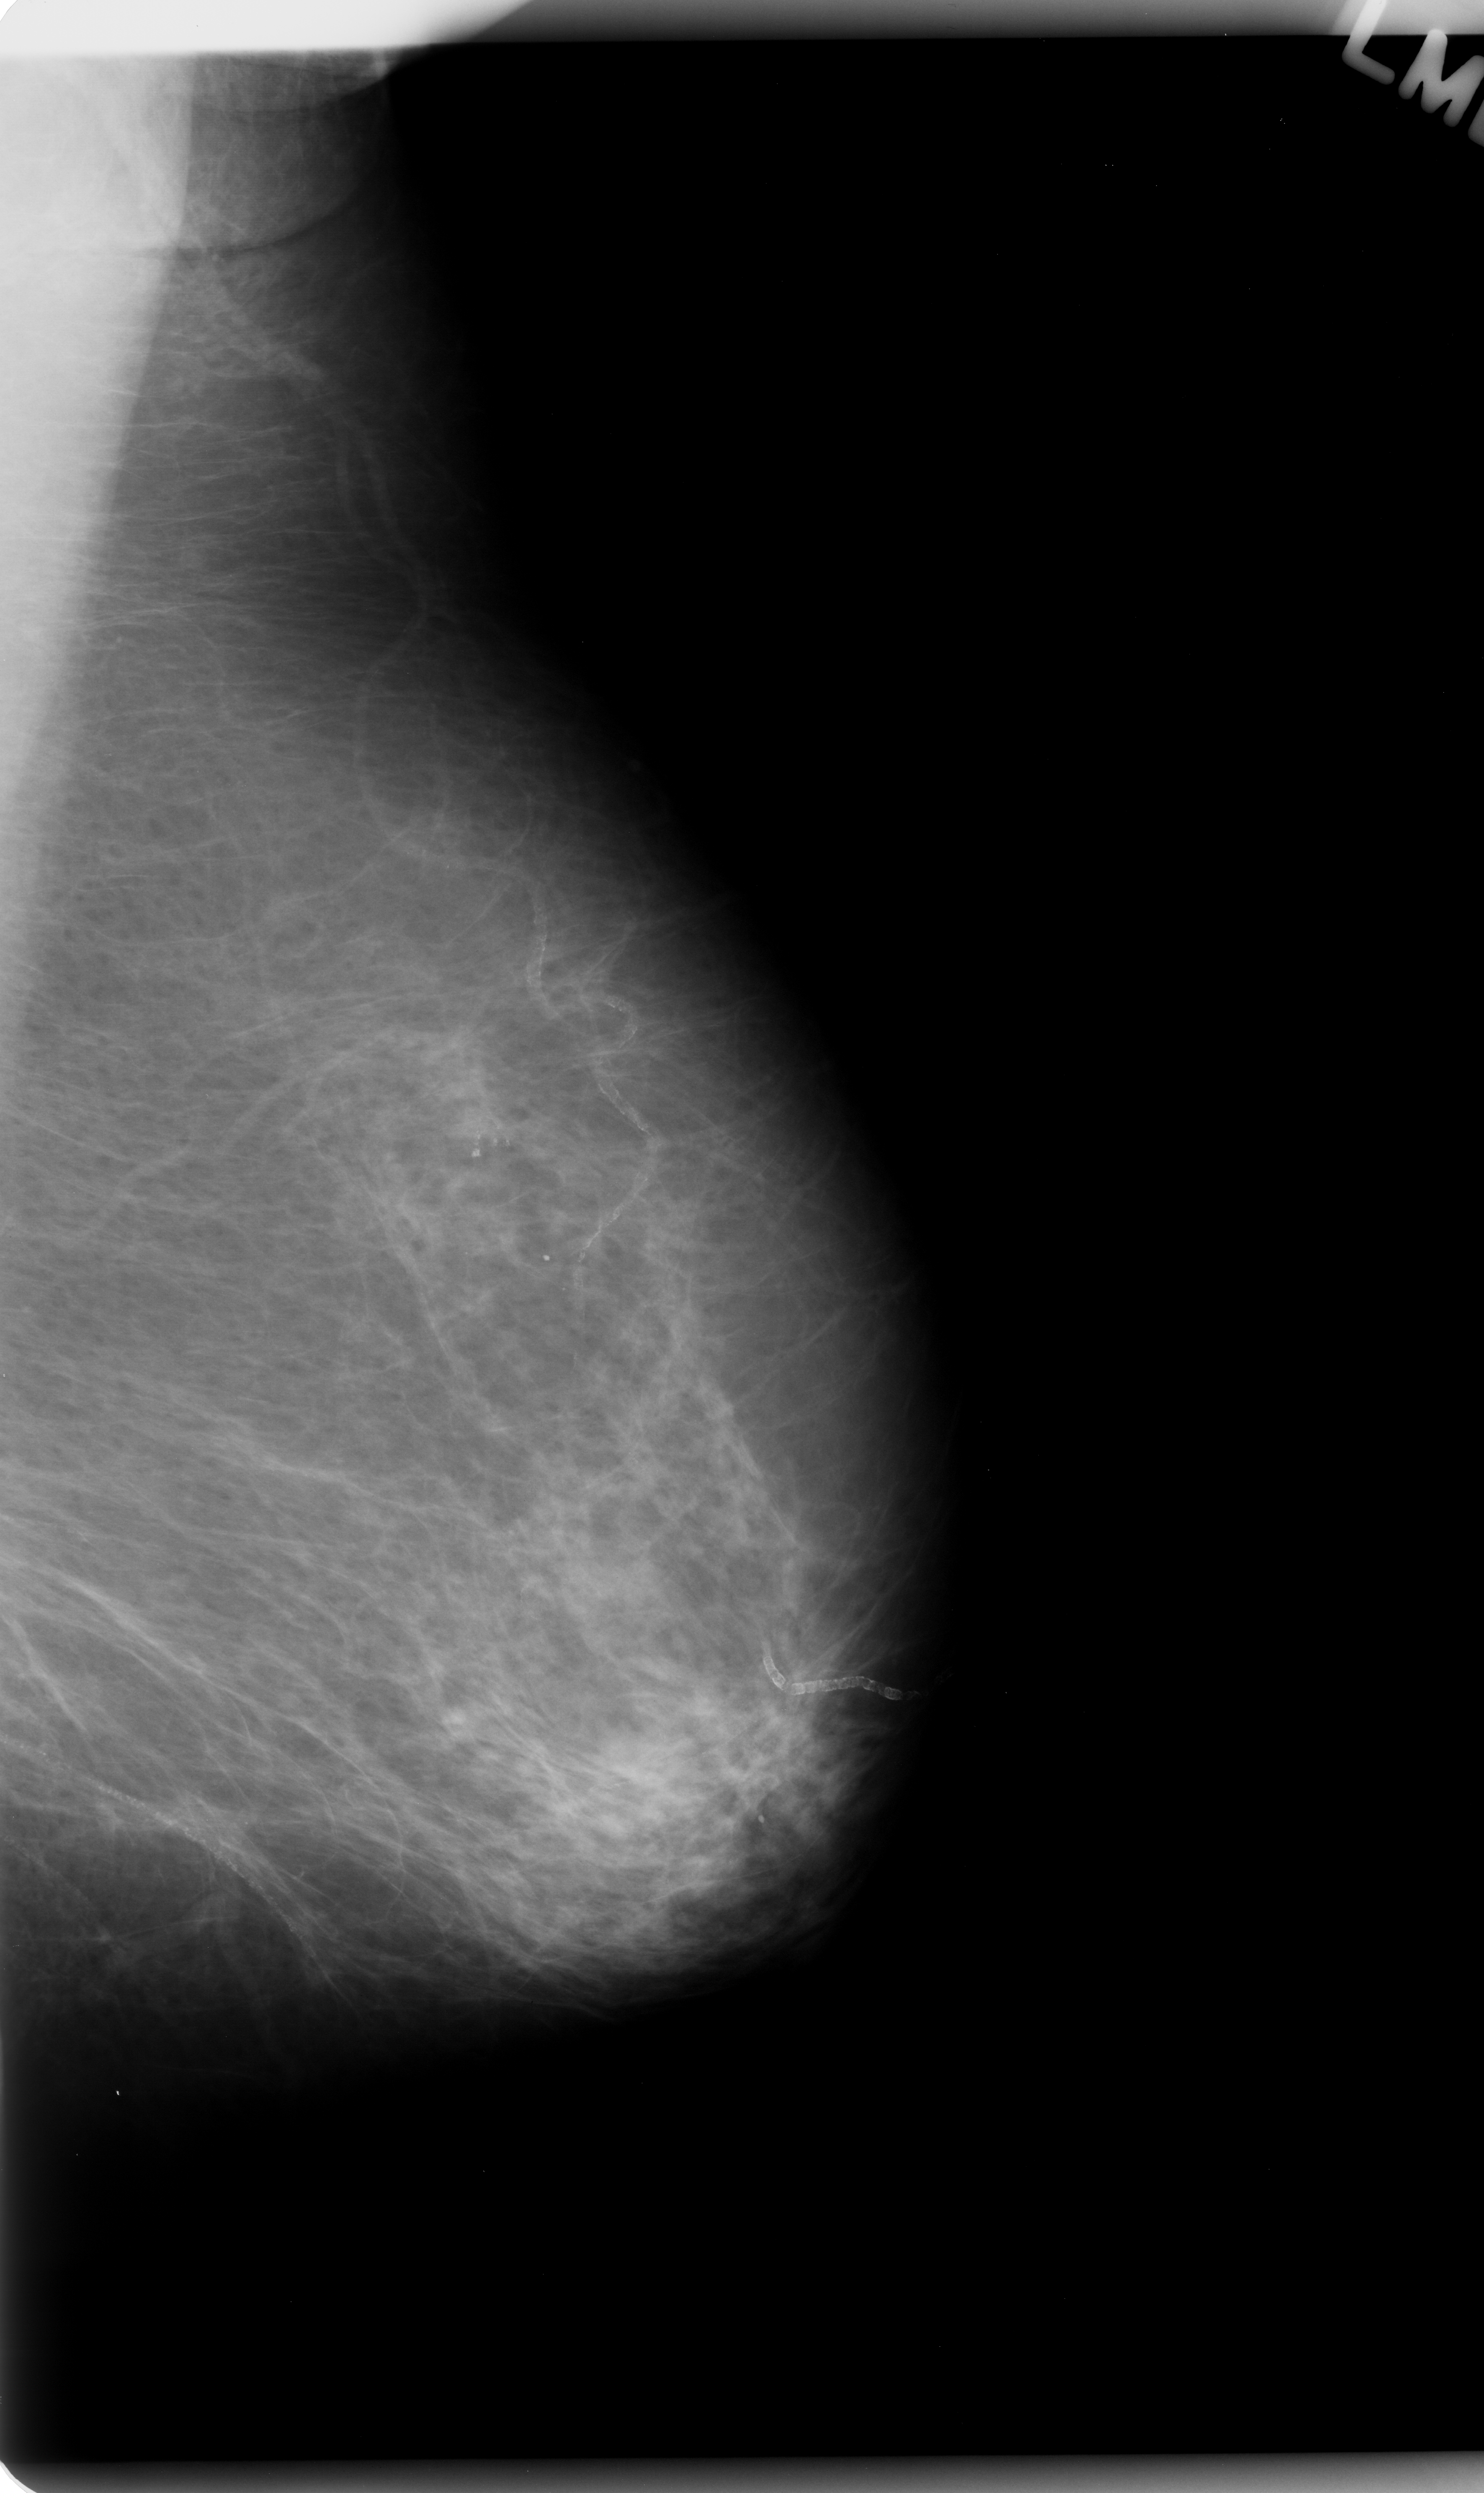
Digitized screen-film mammogram; left breast; mediolateral oblique (MLO) view; BI-RADS breast density category 1 (scale 1–4); 1484 × 2493 image matrix.
Marked abnormalities (boxes around the expert regions of interest):
- calcifications, morphology pleomorphic, distribution clustered; BI-RADS assessment category 4; pathology (as recorded): benign: bounding box (x1, y1, x2, y2) in pixels: (435, 1065, 557, 1204)